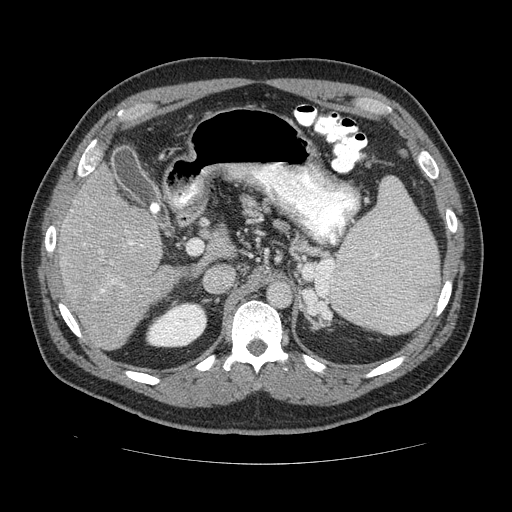
Contrast-enhanced abdominal CT (liver protocol), one axial slice. Slice 77 of 113 in the series (ordered by position). Reconstruction kernel STANDARD. 120 kVp. Soft-tissue window (W 400 / L 40 HU). 2.5 mm slice thickness. 512 × 512 image matrix. Case-level facts recorded for this patient, not image findings: diagnosis: hepatocellular carcinoma (patient treated with transarterial chemoembolisation; whether this scan precedes or follows treatment is not stated here); TNM stage (as recorded): Stage-II; Child-Pugh class: B; tumour differentiation: moderately differentiated; tumour nodularity: multinodular.
Annotated regions visible in this slice (semi-automatically segmented with operator editing):
- liver parenchyma outside the tumour (the mass and vessels are separate outlines, so this box may not span the whole liver): bounding box (x1, y1, x2, y2) in pixels: (50, 164, 224, 350)
- liver vessels: (52, 231, 141, 291)